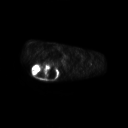
FDG PET of an extremity soft-tissue mass (from a PET/CT study), one axial slice; slice 198 of 267 in the series (ordered by position); 3.27 mm slice thickness; 128 × 128 image matrix. Patient: male, 61 years. From the clinical record (not read from this slice): histological type: pleiomorphic spindle cell undifferentiated; grade: high; site of the primary tumour: right parascapusular.
Outlined on this slice (expert contour drawn on MRI and transferred to this co-registered scan by the dataset authors):
- gross tumour volume including surrounding oedema: box from (x=31, y=63) to (x=60, y=79) px
- gross tumour volume (mass): (x=31, y=63)–(x=58, y=78)